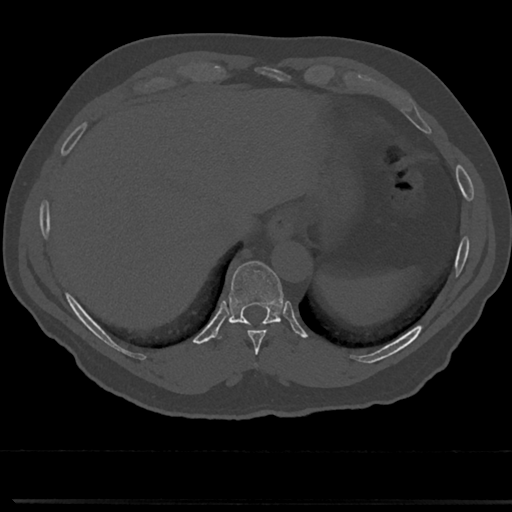
CT including the spine, one axial slice. Position 277 of 817 along the scan axis. Reconstruction kernel Br40s/3. Bone window (W 1800 / L 400 HU). 512 × 512 image matrix. Male patient, age 61 years. Case-level facts recorded for this patient, not image findings: primary cancer: prostate.
Annotated regions visible in this slice (semi-automatic segmentation, software-assisted and operator-edited):
- T10 vertebra: box from (x=230, y=262) to (x=281, y=323) px
- T8 vertebra: (x=237, y=319)–(x=280, y=370)
- T9 vertebra: (x=228, y=284)–(x=287, y=348)